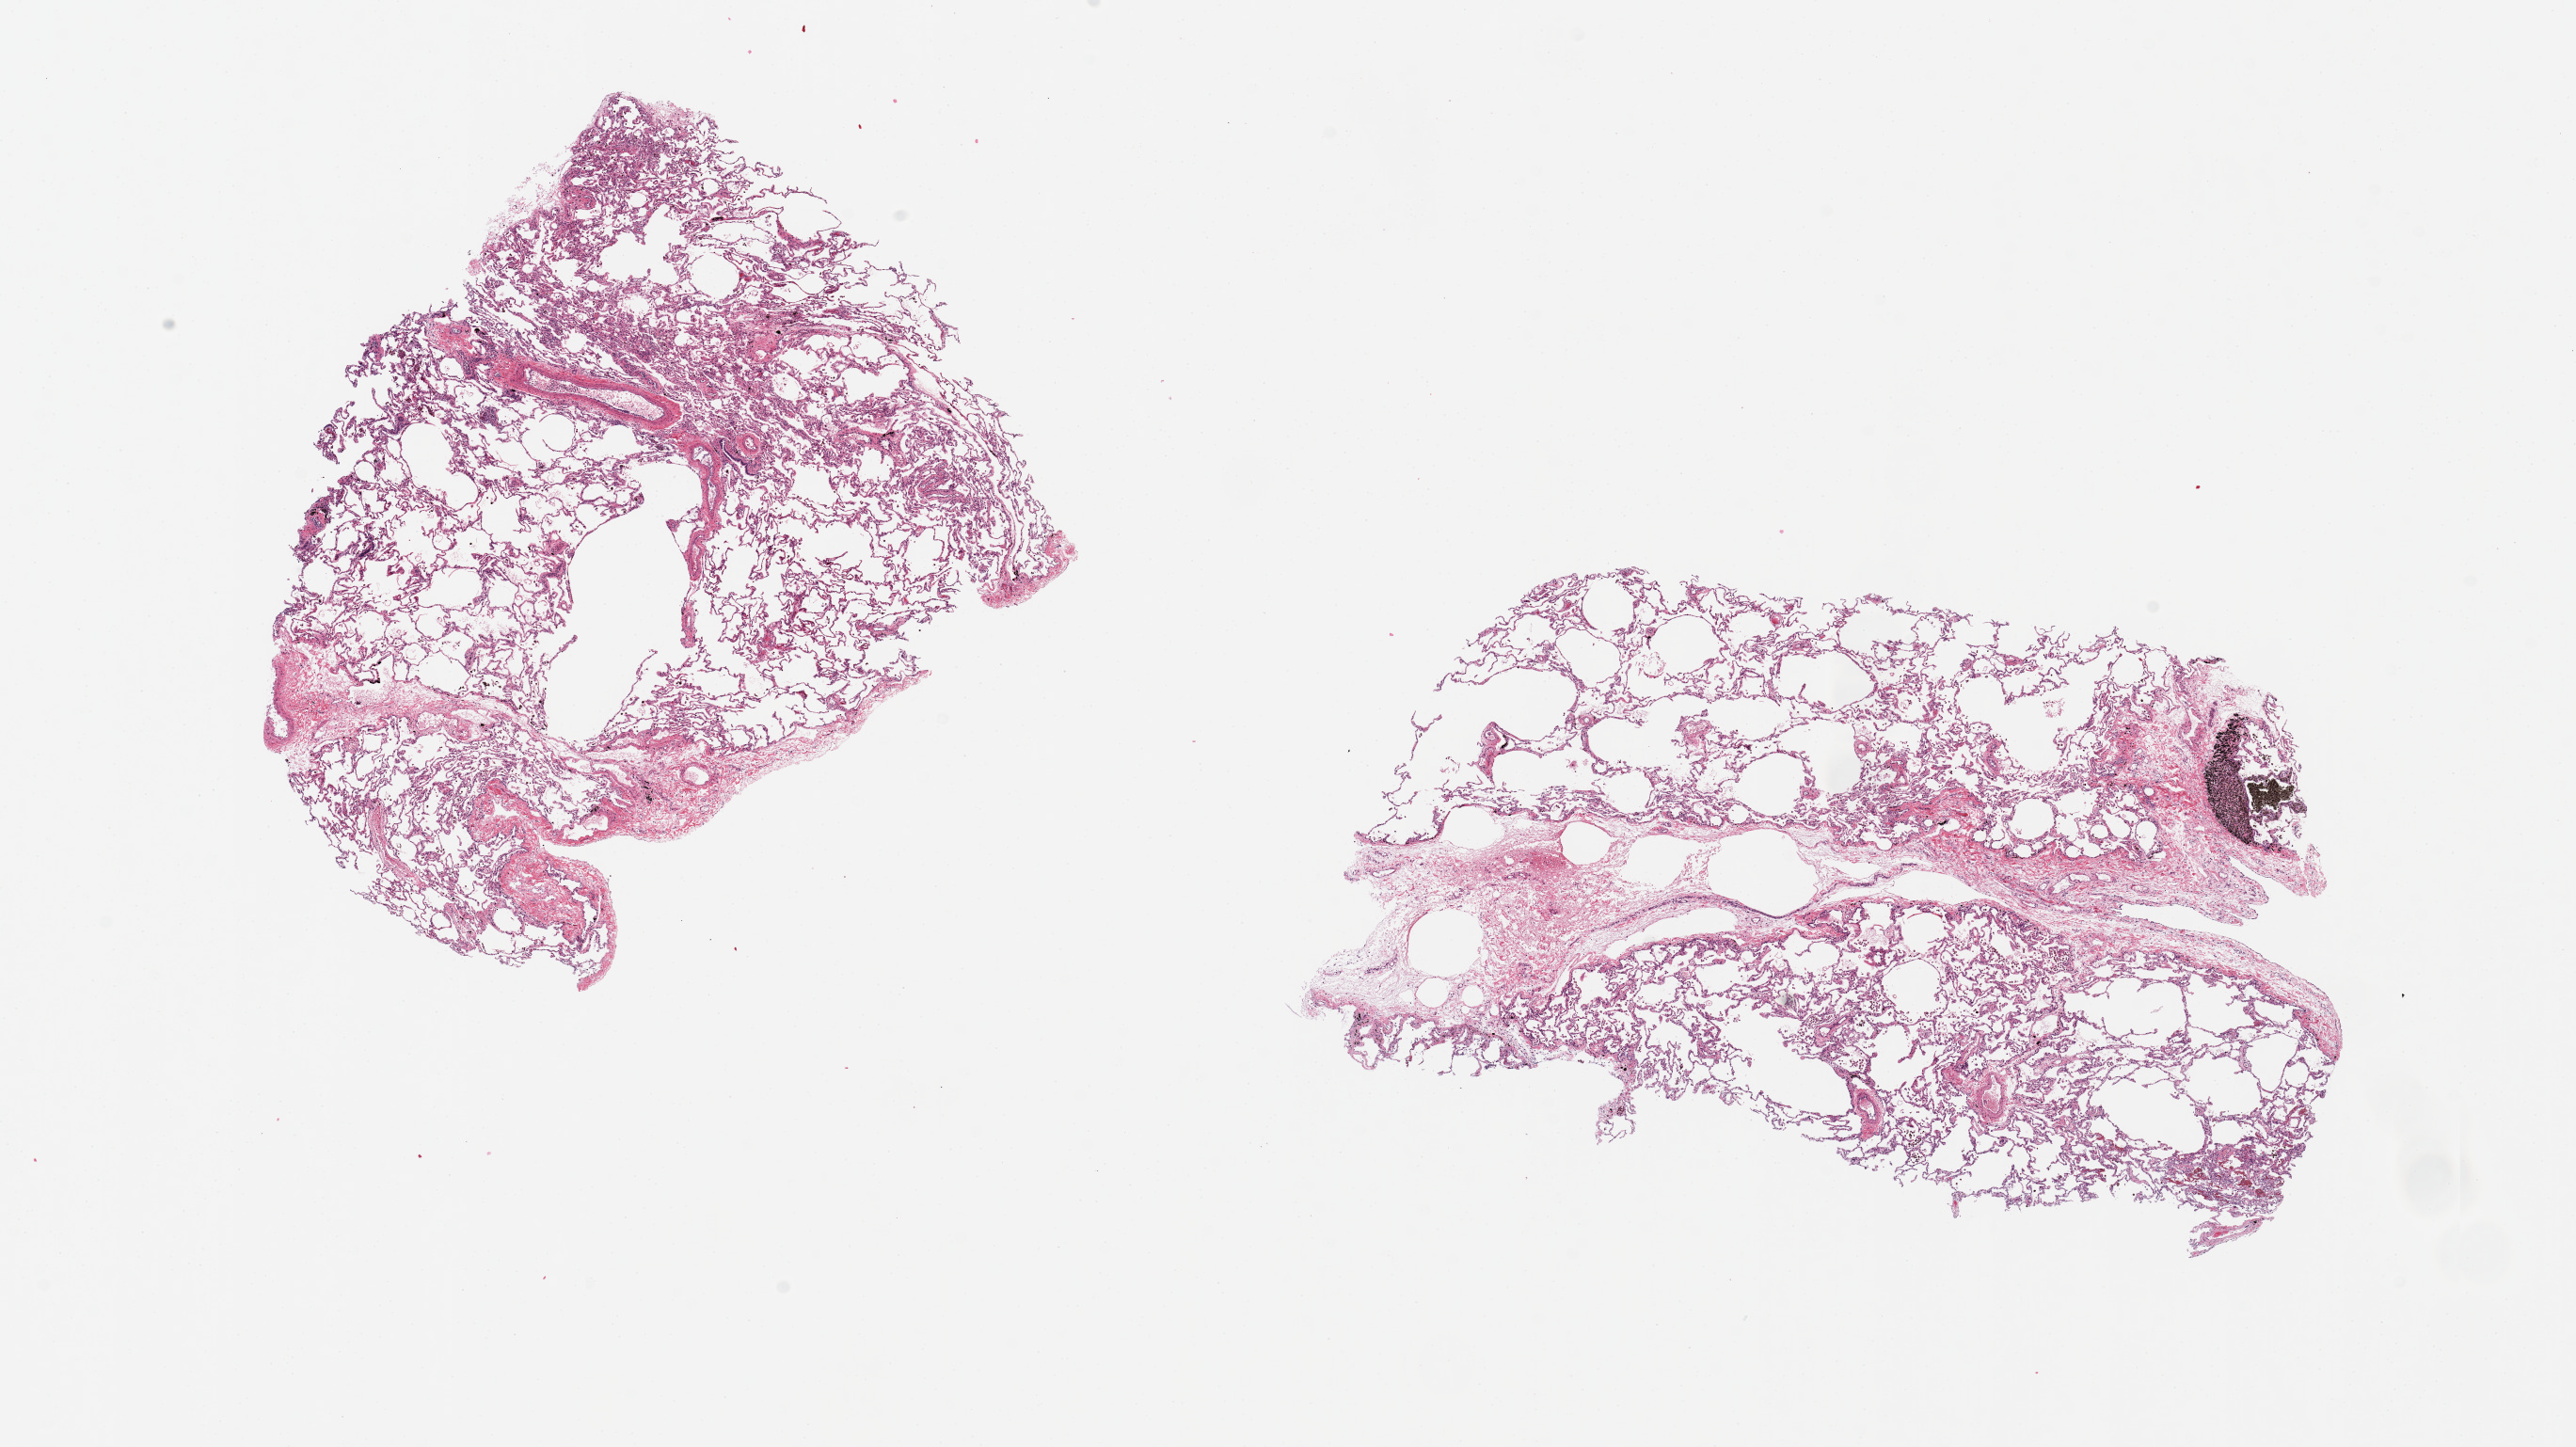
H&E whole-slide image — whole scanned area (about 21.7 x 12.2 mm, slide scanned at 20x) shown as a low-resolution overview; PAXgene-fixed, paraffin-embedded tissue; target tissue: lung; donor tissue sample.
Reviewer comment on this tissue sample: 2 pieces, 8.5x5 & 7x5.5mm; emphysema; carbon laden macrophages focally in lymphoid nodule.